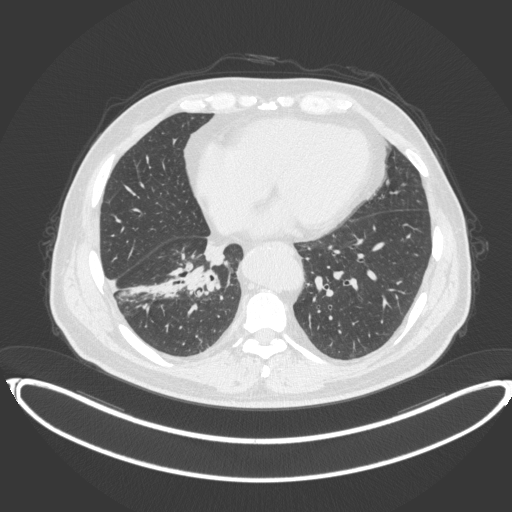
Chest CT, one axial slice; slice 147 of 383 in the series (ordered by position); lung window (W 1500 / L -600 HU); 1 mm slice thickness; 512 × 512 image matrix. Patient: male, 61 years. Case-level facts recorded for this patient, not image findings: clinical TNM (as recorded): T1b N1 M0.
Outlined on this slice (rectangle marked by the reading radiologist):
- lung tumour (recorded histology: squamous cell carcinoma): box from (x=184, y=266) to (x=224, y=300) px